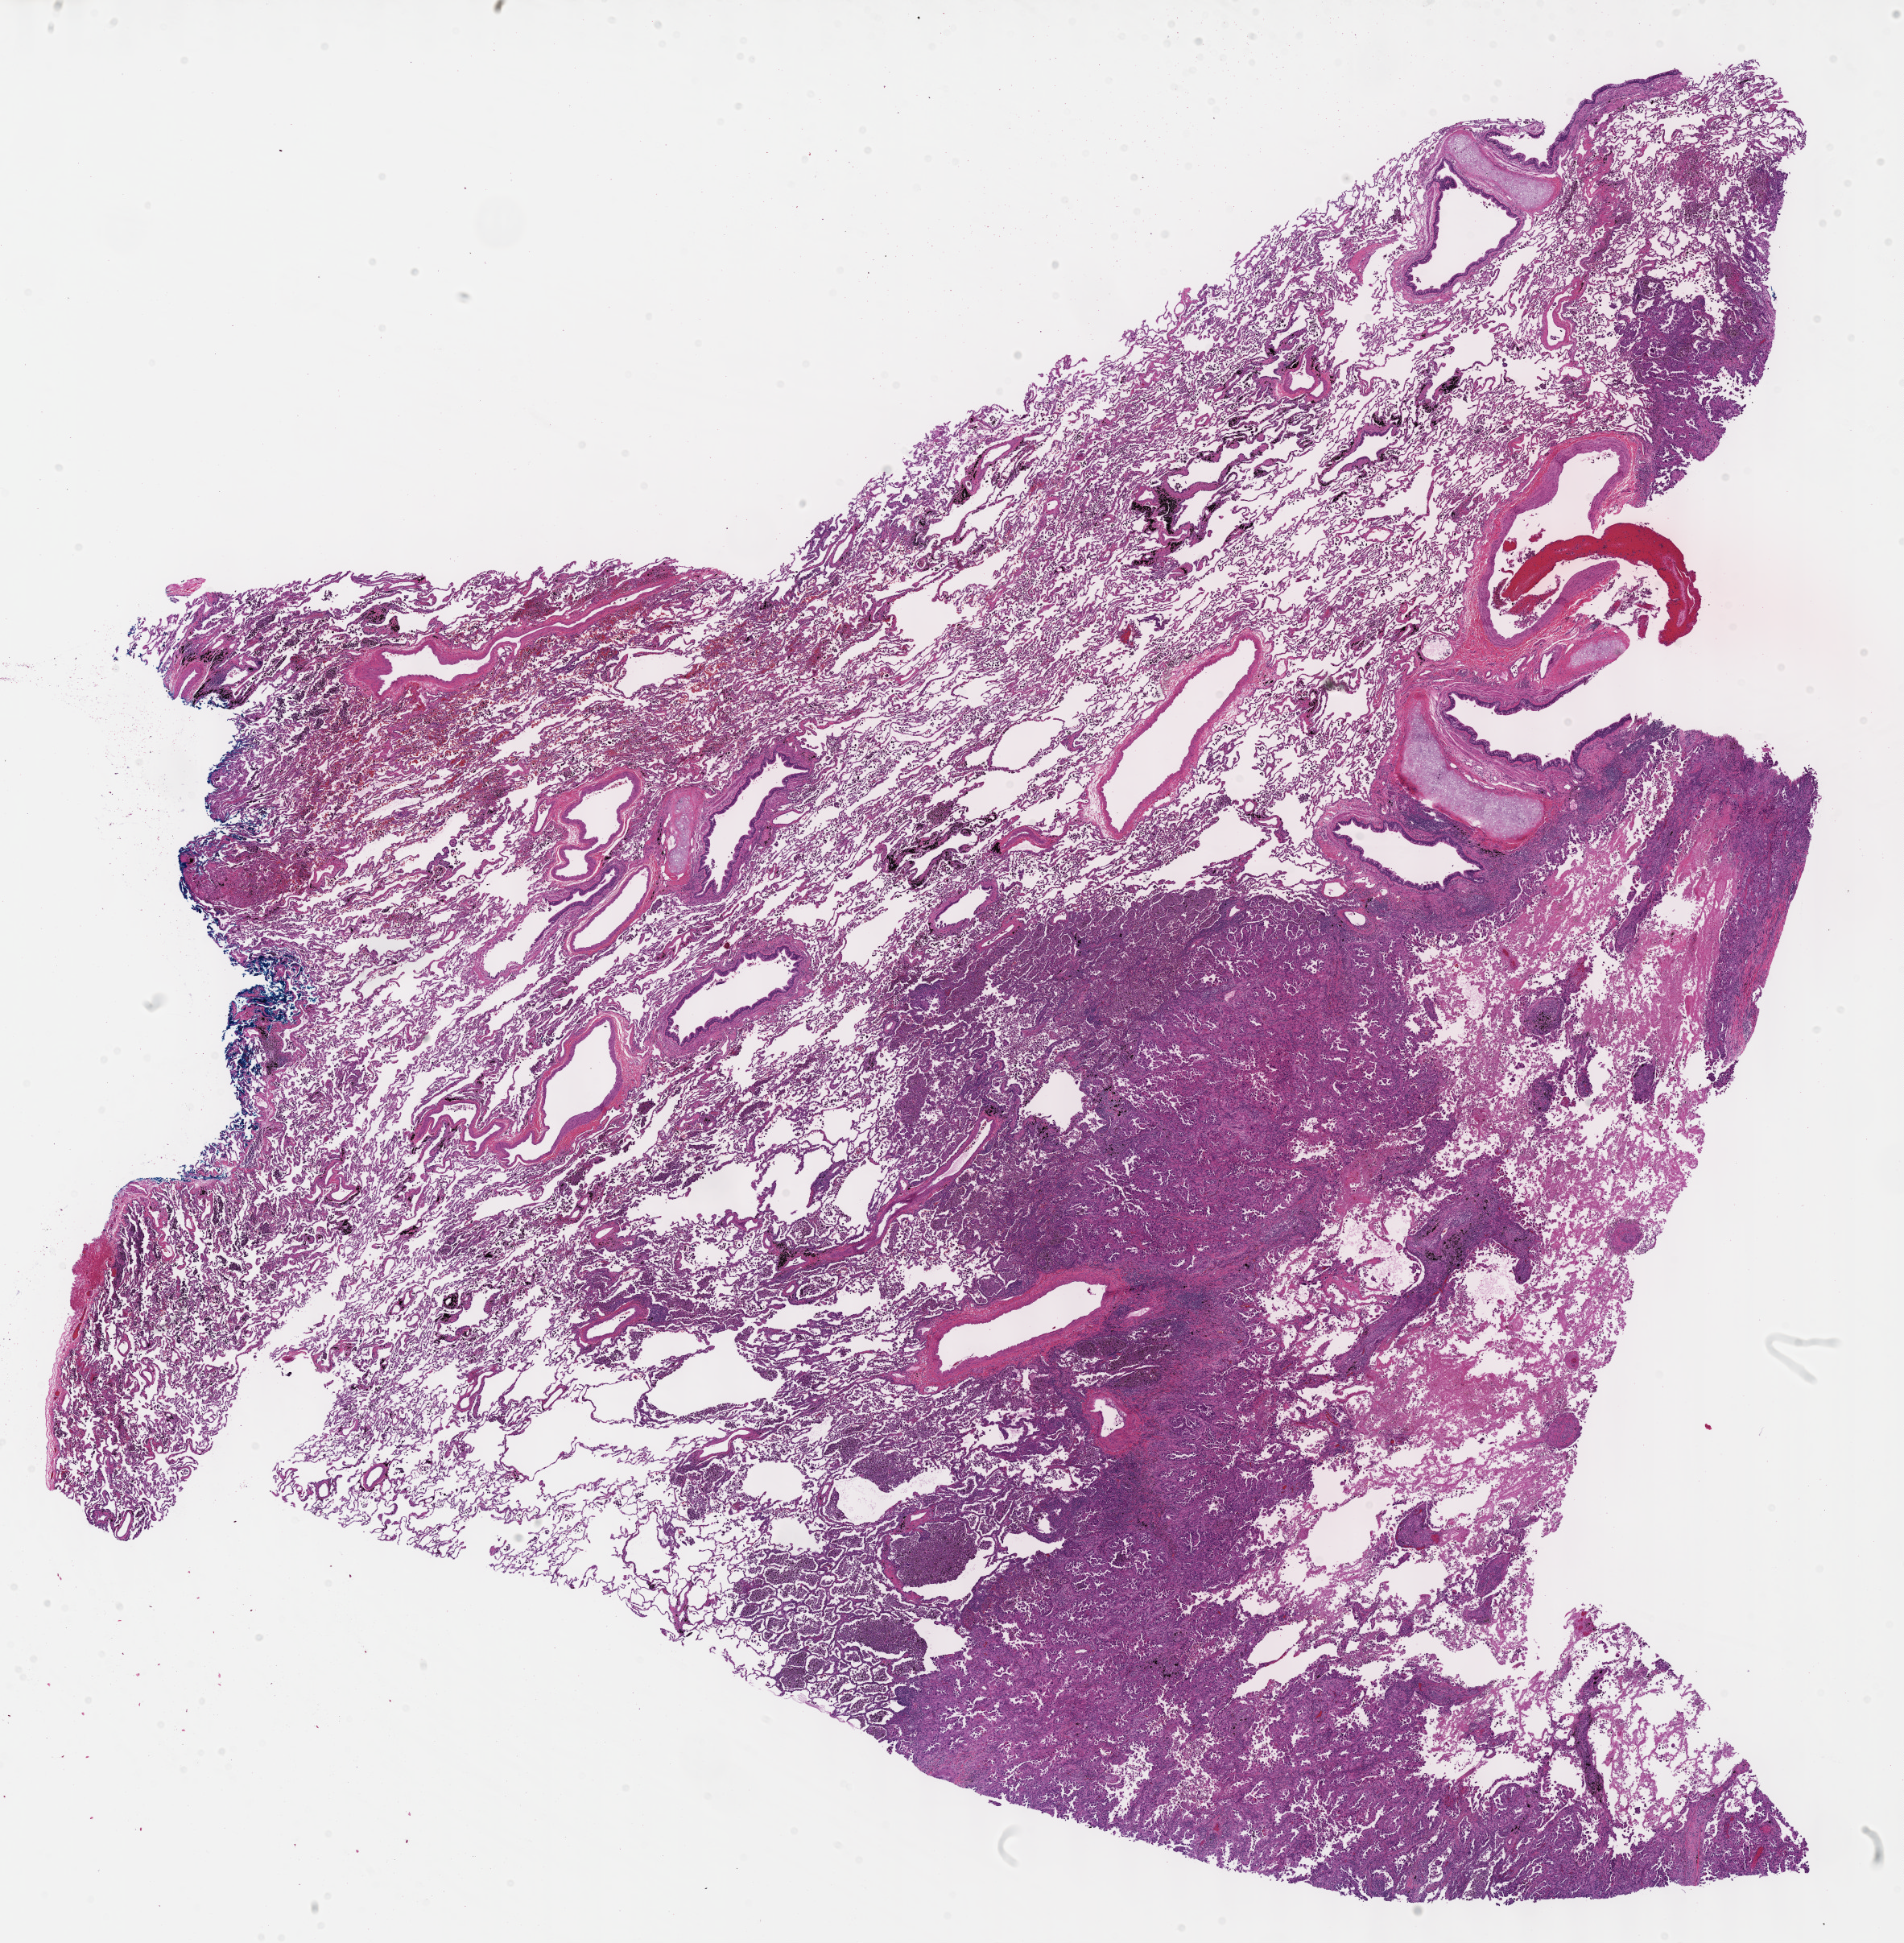
Digitized H&E-stained tissue section (whole slide) — low-resolution overview of the scanned area, about 19.1 x 19.5 mm. FFPE section. Lung, primary tumour sample. Female patient; age at initial diagnosis 39 years.
• laterality: left
• histologic diagnosis: Papillary adenocarcinoma, NOS (upper lobe, lung)
• AJCC pathologic stage: IA (6th edition)